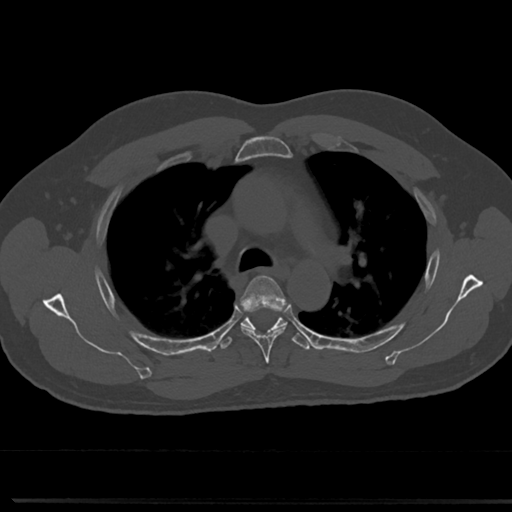
CT including the spine, one axial slice. Slice 527 of 817 in the series (ordered by position). Reconstruction kernel Br40s/3. 120 kVp. Bone window (W 1800 / L 400 HU). 0.5 mm slice thickness. 512 × 512 image matrix, field of view 355 × 355 mm. Patient: male, 61 years. From the clinical record (not read from this slice): primary cancer: prostate.
Outlined on this slice (semi-automatically segmented with operator editing):
- T4 vertebra: bounding box [x1, y1, x2, y2] px = [238, 276, 289, 358]
- T5 vertebra: [242, 320, 285, 329]